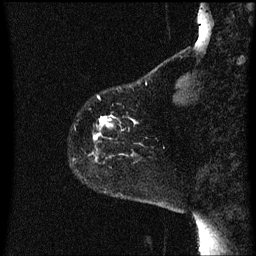
Breast MRI (dynamic contrast-enhanced), one sagittal slice; slice 10 of 60 in the series (ordered by position); dynamic contrast-enhanced series, image 2 of 3 at this slice position (ordered by acquisition); 1.5 T; TE 4.2 ms, TR 8 ms; 2 mm slice thickness; 256 × 256 image matrix, field of view 200 × 200 mm. Patient: female, 60 years.
Annotated regions visible in this slice (semi-automatic segmentation, software-assisted and operator-edited):
- analysis volume of interest (the breast-tissue region the enhancement analysis was run in; not a lesion): bounding box [x1, y1, x2, y2] px = [94, 96, 142, 163]
- tumour enhancement mask (voxels above the 70 % enhancement threshold inside the analysis volume of interest): [94, 116, 136, 141]